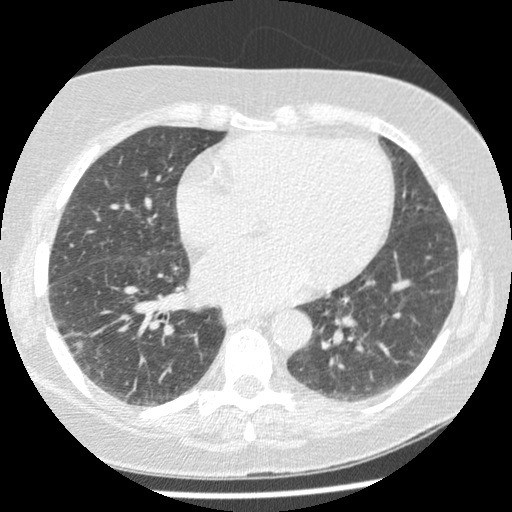
Low-dose screening chest CT, one axial slice; position 102 of 241 along the scan axis; reconstruction kernel STANDARD; 120 kVp; lung window (W 1500 / L -600 HU); 1.25 mm slice thickness; 512 × 512 image matrix, field of view 305 × 305 mm.
Outlined on this slice (outlined manually by an expert reader):
- lesion 1 (tumor, lower lobe of right lung): bounding box <73,340,83,354> (left, top, right, bottom; pixels)